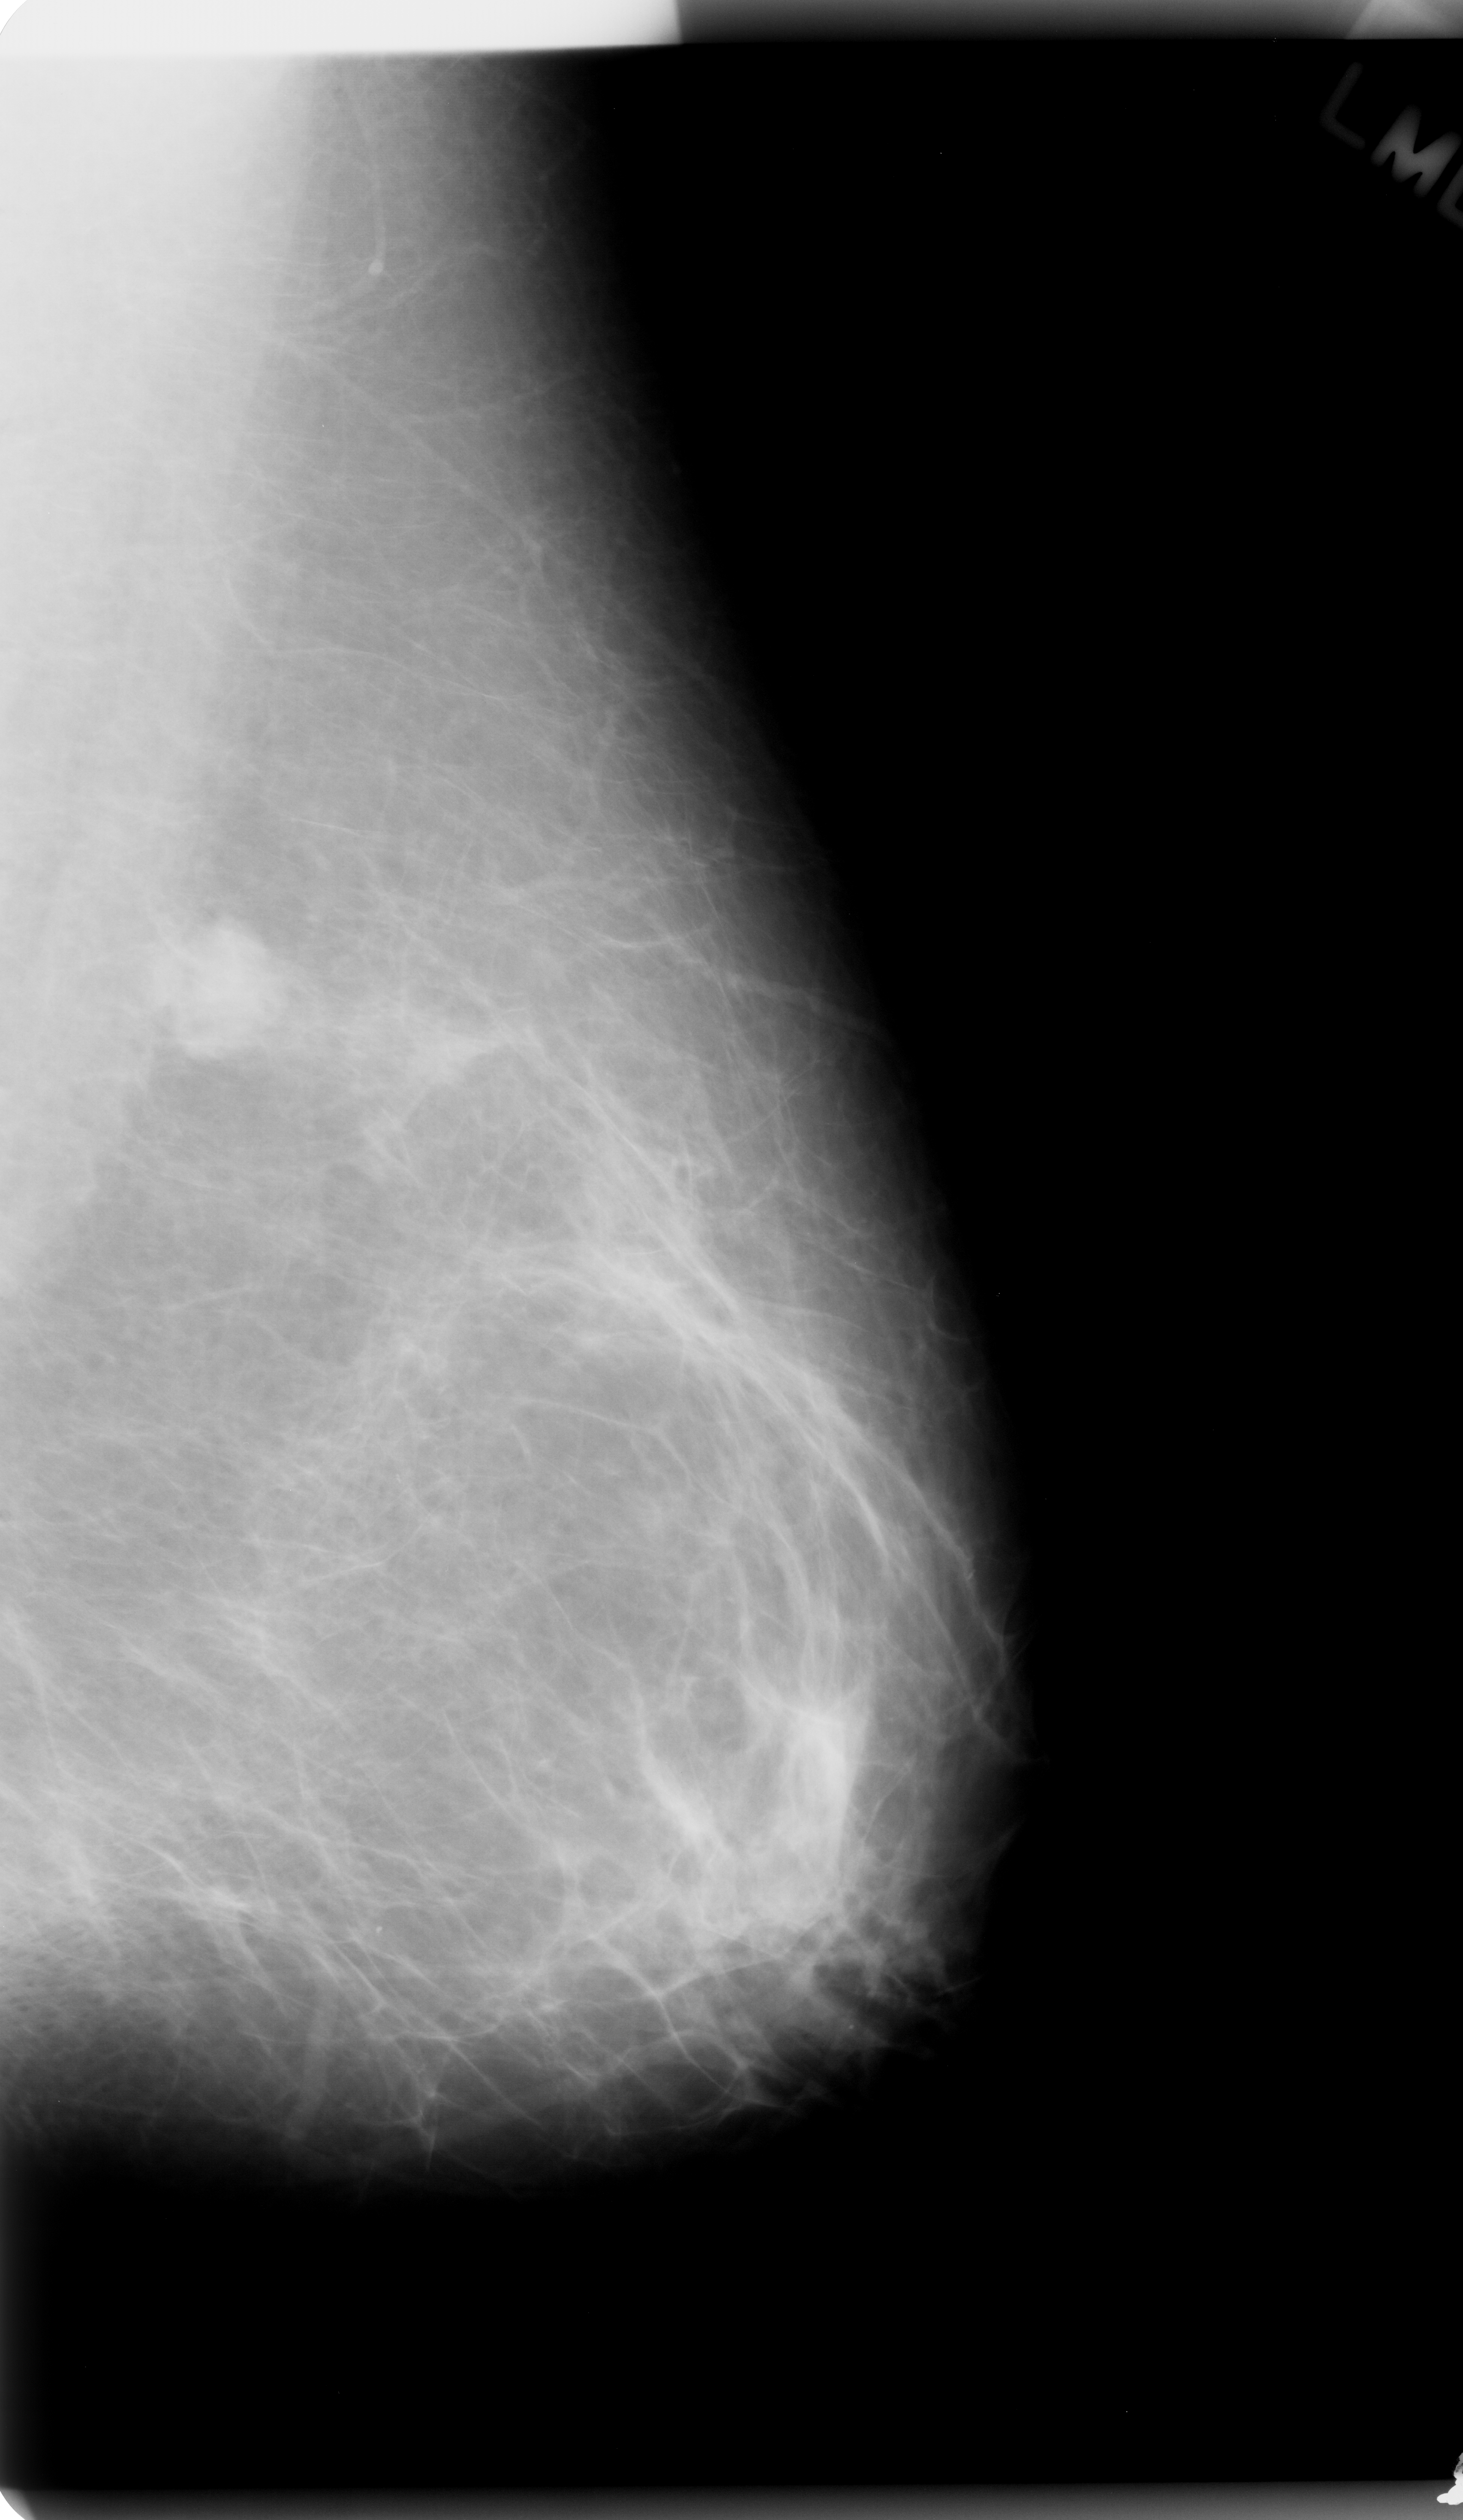
Digitized screen-film mammogram. Left breast. Mediolateral oblique (MLO) view. Breast composition: almost entirely fatty (BI-RADS density category 1 of 4). 1463 × 2520 image matrix.
Marked abnormalities (boxes around the expert regions of interest):
- mass, shape oval, margins microlobulated; BI-RADS assessment category 5; subtlety rating 5 on a 1 (subtle) to 5 (obvious) scale; pathology (as recorded): malignant: box from (x=149, y=910) to (x=298, y=1068) px